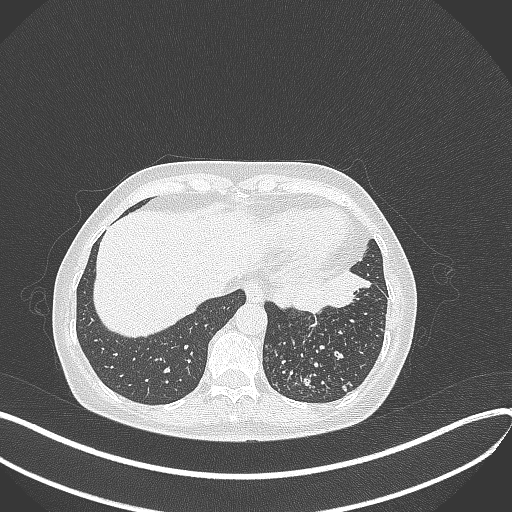
Chest CT, one axial slice; slice 91 of 429 in the series (ordered by position); lung window (W 1500 / L -600 HU); 512 × 512 image matrix, field of view 400 × 400 mm. Patient: female, 63 years. From the clinical record (not read from this slice): clinical TNM (as recorded): T1b N0 M0.
Structures marked on this image (bounding box drawn by a radiologist):
- lung tumour (recorded histology: adenocarcinoma): box from (x=269, y=269) to (x=371, y=313) px